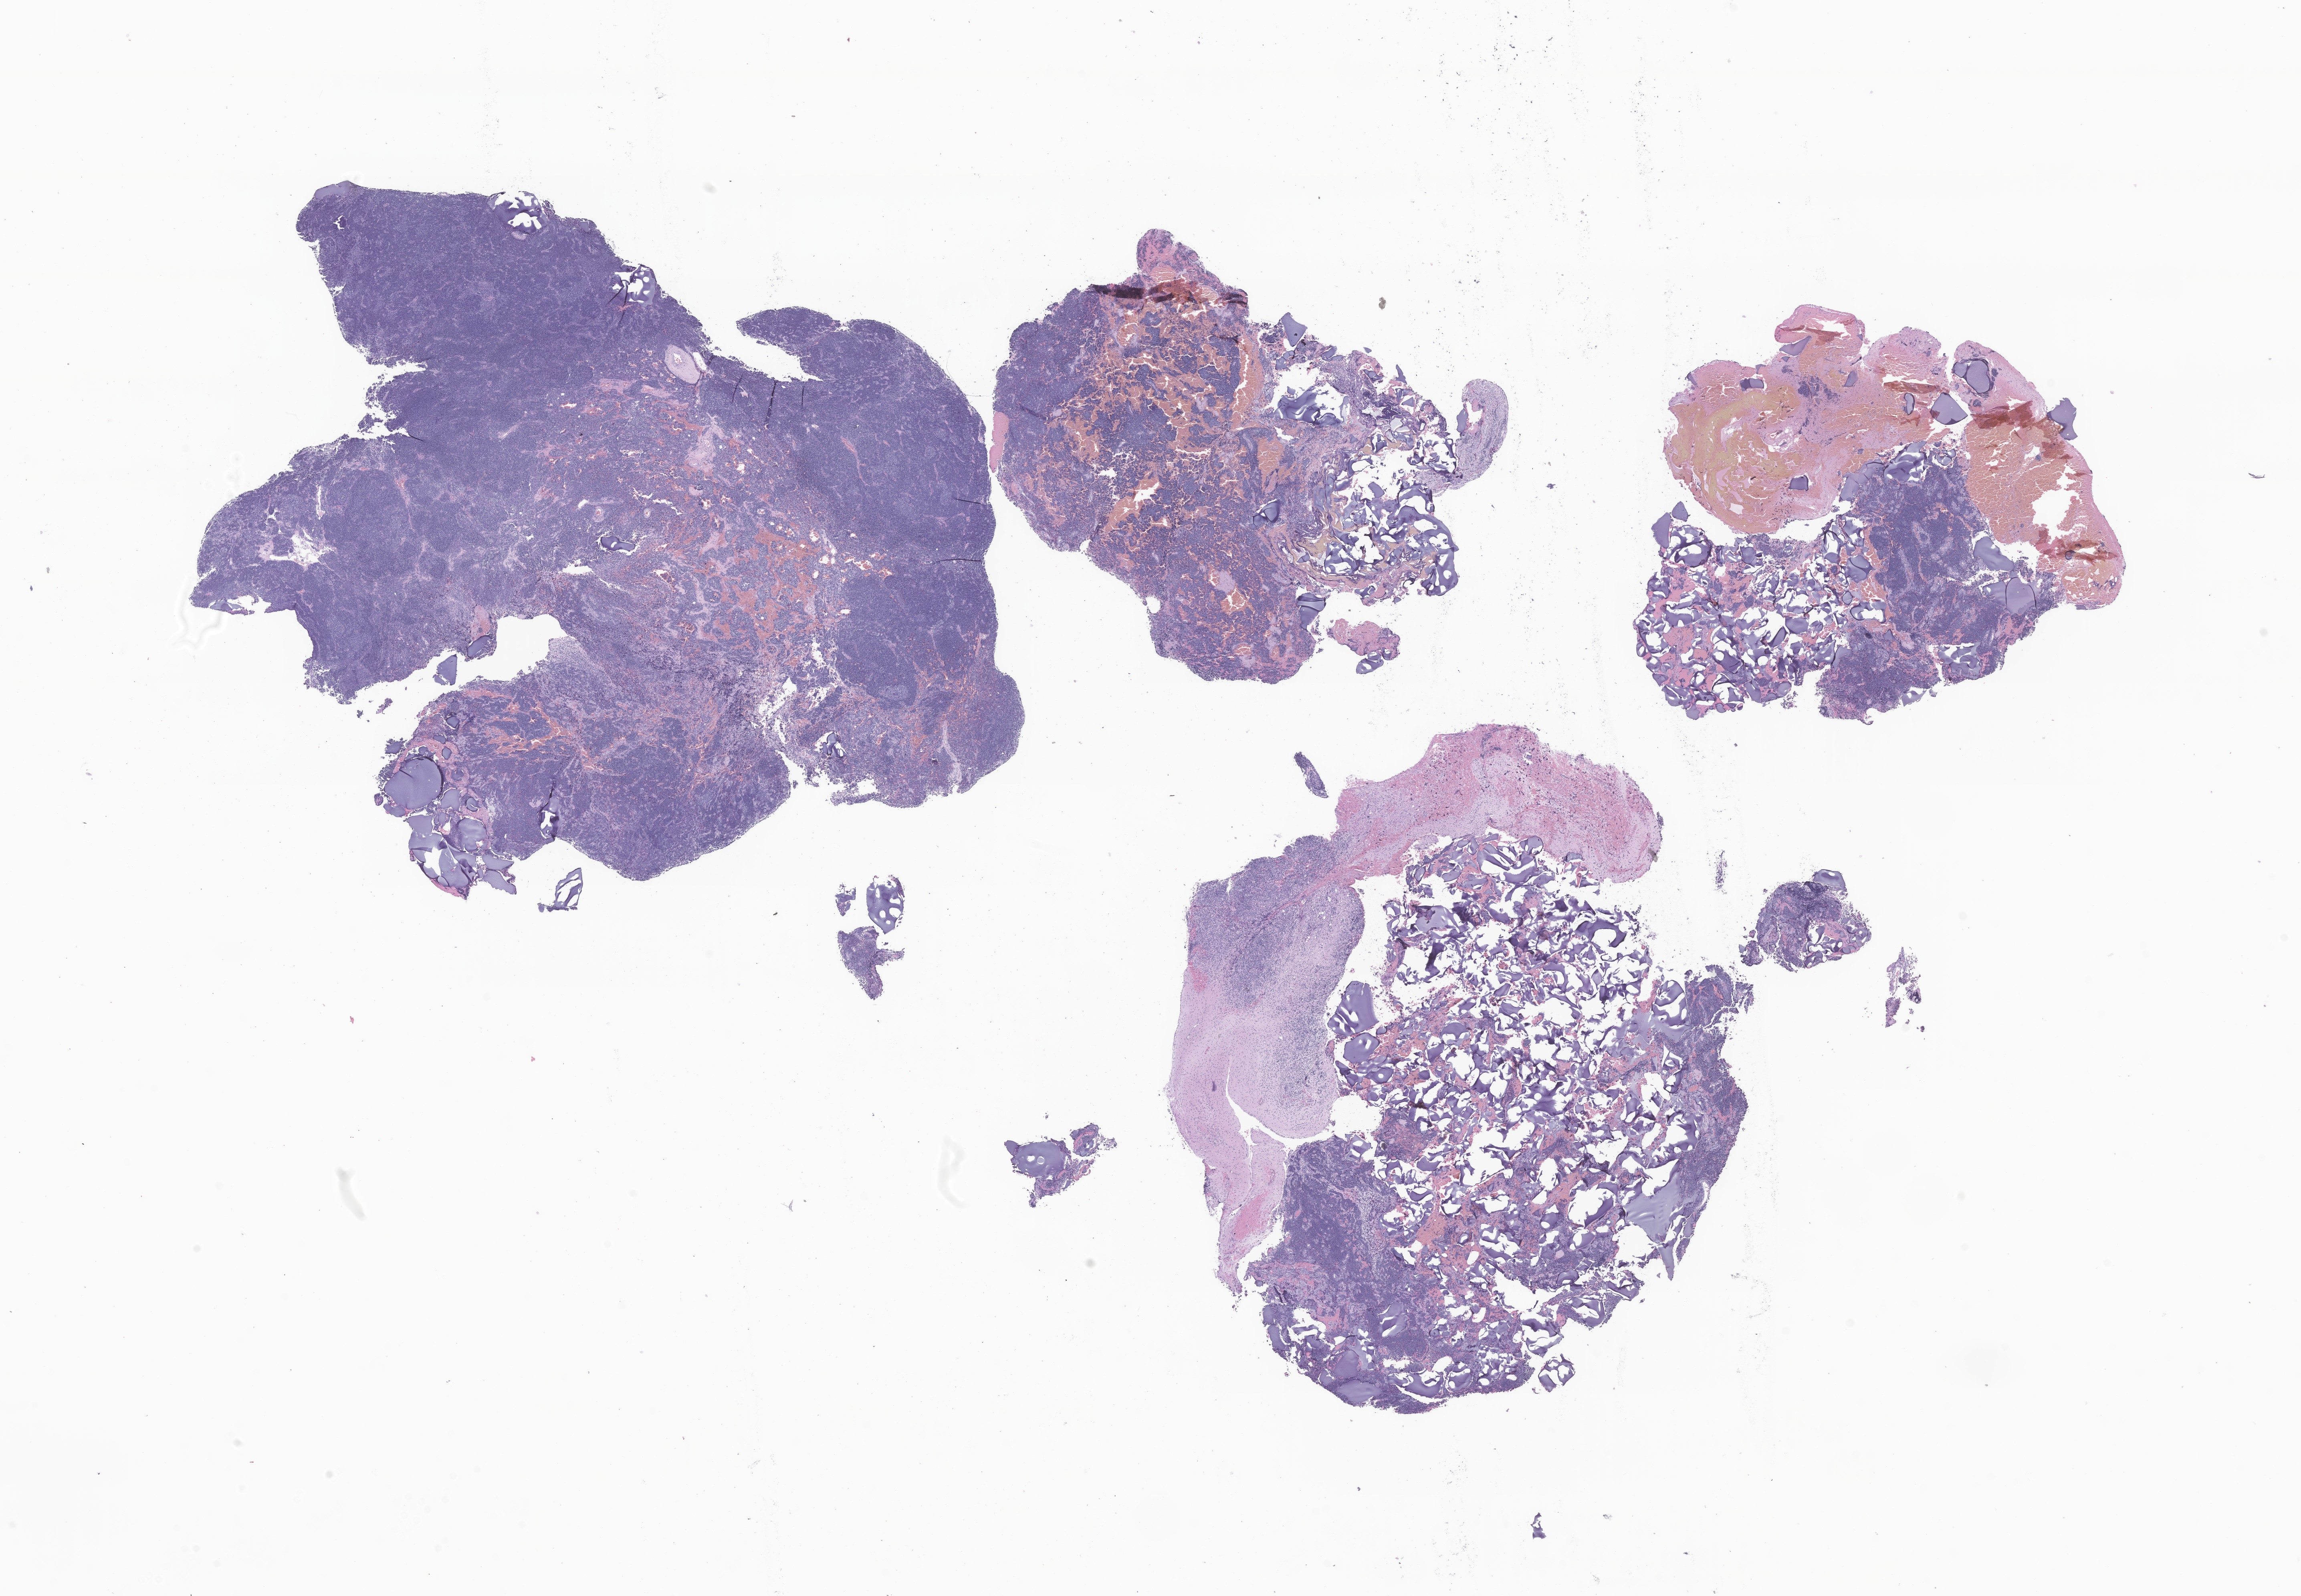
Digitized H&E-stained section of tumor tissue from the brain — whole scanned area (about 24.2 x 16.8 mm) shown as a low-resolution overview, formalin-fixed paraffin-embedded section. Patient male; age 215 months.
Recorded diagnosis: Medulloblastoma, NOS.